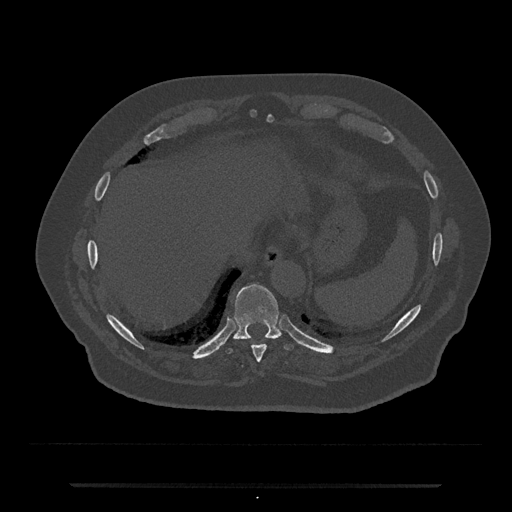
CT including the spine, one axial slice; slice 728 of 797 in the series (ordered by position); reconstruction kernel Br40s/3; 120 kVp; bone window (W 1800 / L 400 HU); 0.5 mm slice thickness; 512 × 512 image matrix, field of view 434 × 434 mm. Patient: male, 80 years. From the clinical record (not read from this slice): primary cancer: prostate; vertebrae with lytic lesions (as recorded): L1, T11.
Annotated regions visible in this slice (semi-automatic segmentation, software-assisted and operator-edited):
- T10 vertebra: box from (x=227, y=284) to (x=294, y=354) px
- T9 vertebra: (x=252, y=344)–(x=266, y=363)